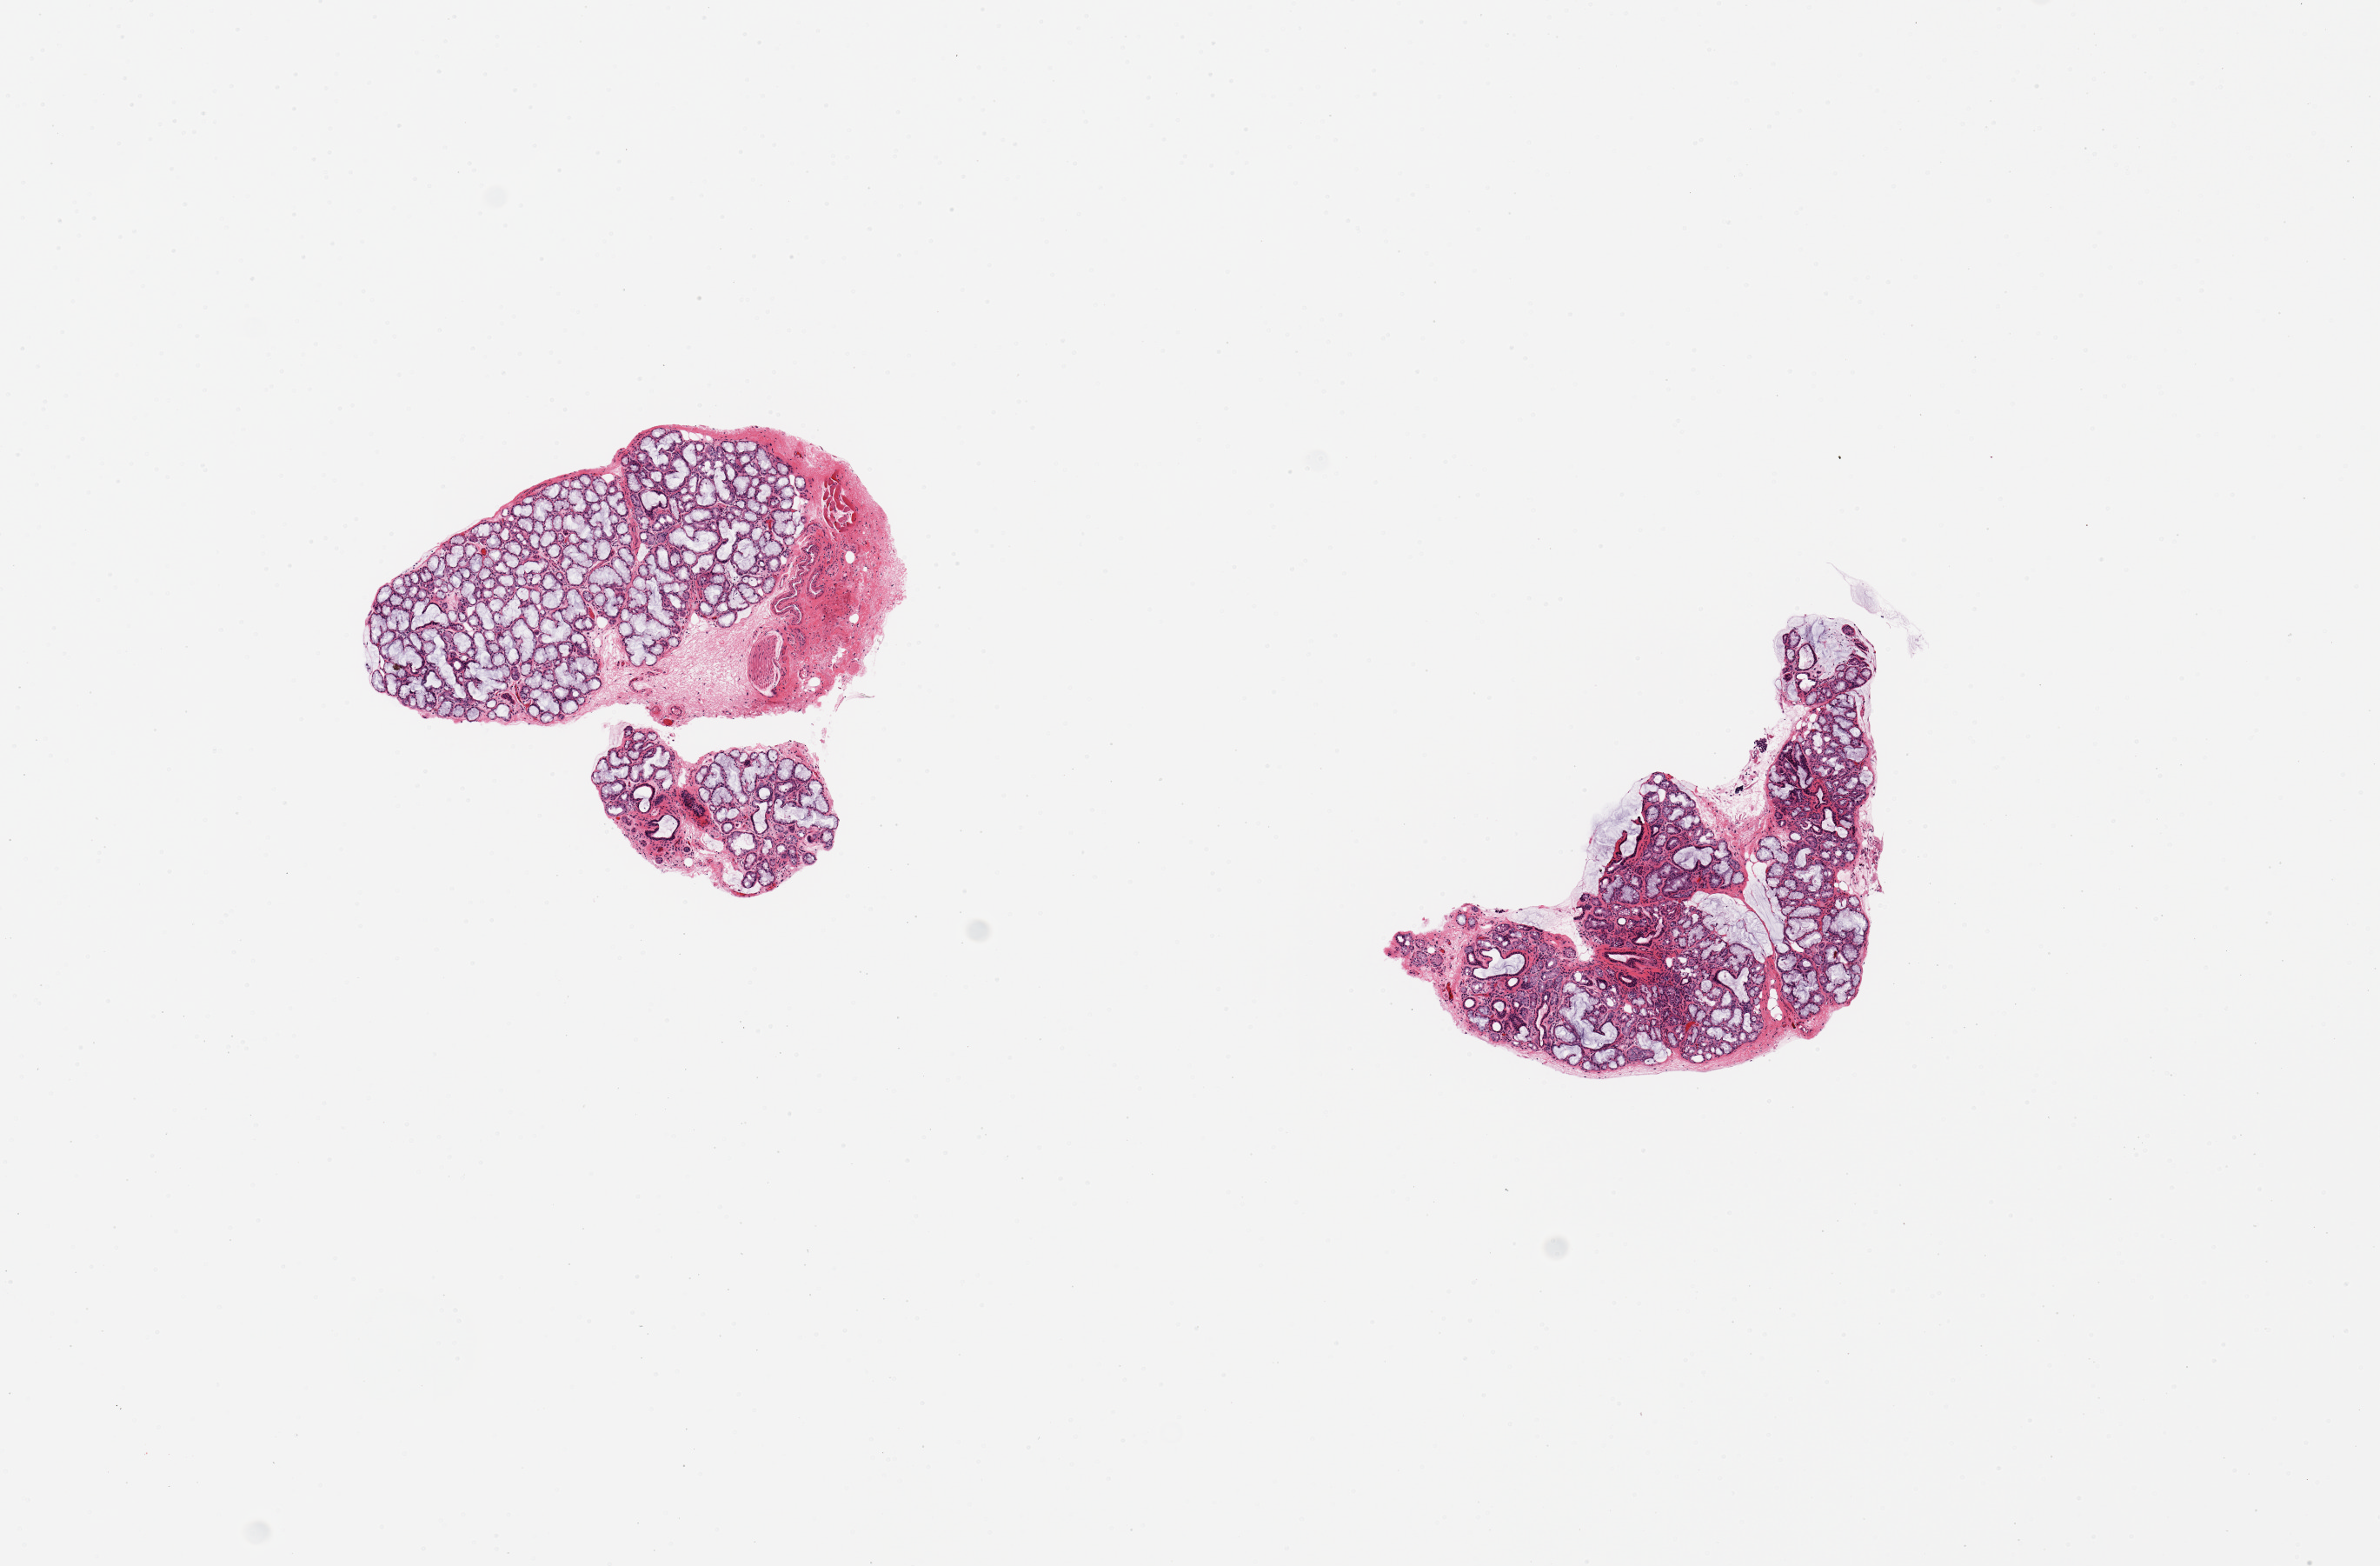
Digitized hematoxylin and eosin (H&E)-stained section, brightfield — shown as a low-resolution overview of the whole scanned area (about 10.8 x 7.1 mm); PAXgene-fixed, paraffin-embedded tissue; sampled site (target tissue): minor salivary gland; donor tissue sample. Donor: male.
Reviewer comment on this tissue sample: 2 pieces, excellent specimens; glandular parenchmyma is ~80% total tisssue.